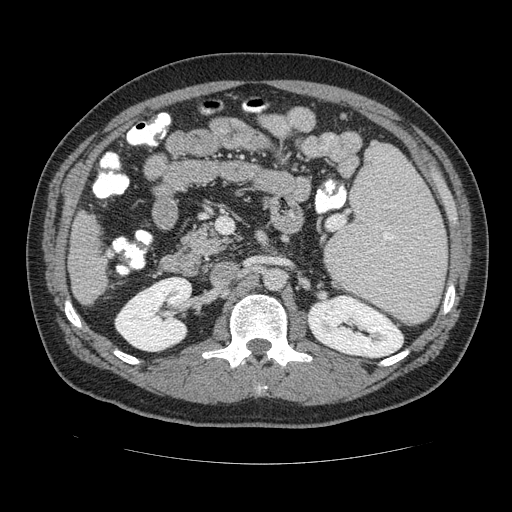
Contrast-enhanced abdominal CT (liver protocol), one axial slice; slice 54 of 113 in the series (ordered by position); reconstruction kernel STANDARD; 120 kVp; soft-tissue window (W 400 / L 40 HU); 2.5 mm slice thickness; 512 × 512 image matrix, field of view 400 × 400 mm. Case-level facts recorded for this patient, not image findings: diagnosis: hepatocellular carcinoma (patient treated with transarterial chemoembolisation; whether this scan precedes or follows treatment is not stated here); TNM stage (as recorded): Stage-II.
Annotated regions visible in this slice (semi-automatically segmented with operator editing):
- liver parenchyma outside the tumour (the mass and vessels are separate outlines, so this box may not span the whole liver): bounding box <66,208,108,306> (left, top, right, bottom; pixels)